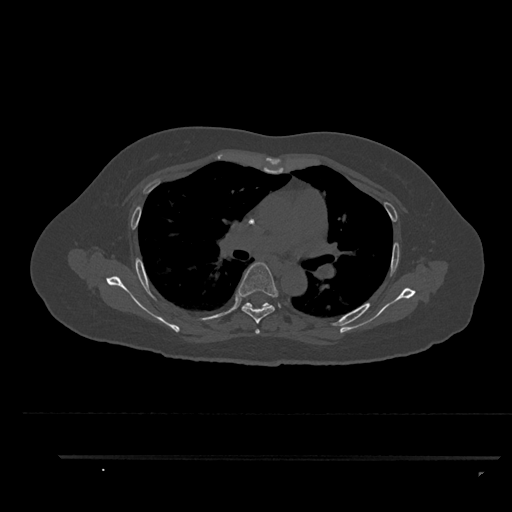
CT including the spine, one axial slice. Slice 594 of 797 in the series (ordered by position). 120 kVp. Bone window (W 1800 / L 400 HU). 0.5 mm slice thickness. 512 × 512 image matrix, field of view 408 × 408 mm. Female patient, age 44 years. Case-level facts recorded for this patient, not image findings: primary cancer: renal; vertebrae with lytic lesions (as recorded): L1.
Structures marked on this image (semi-automatic segmentation, software-assisted and operator-edited):
- T4 vertebra: bounding box (x1, y1, x2, y2) in pixels: (255, 329, 260, 334)
- T5 vertebra: (238, 262, 278, 324)
- T6 vertebra: (242, 302, 273, 309)